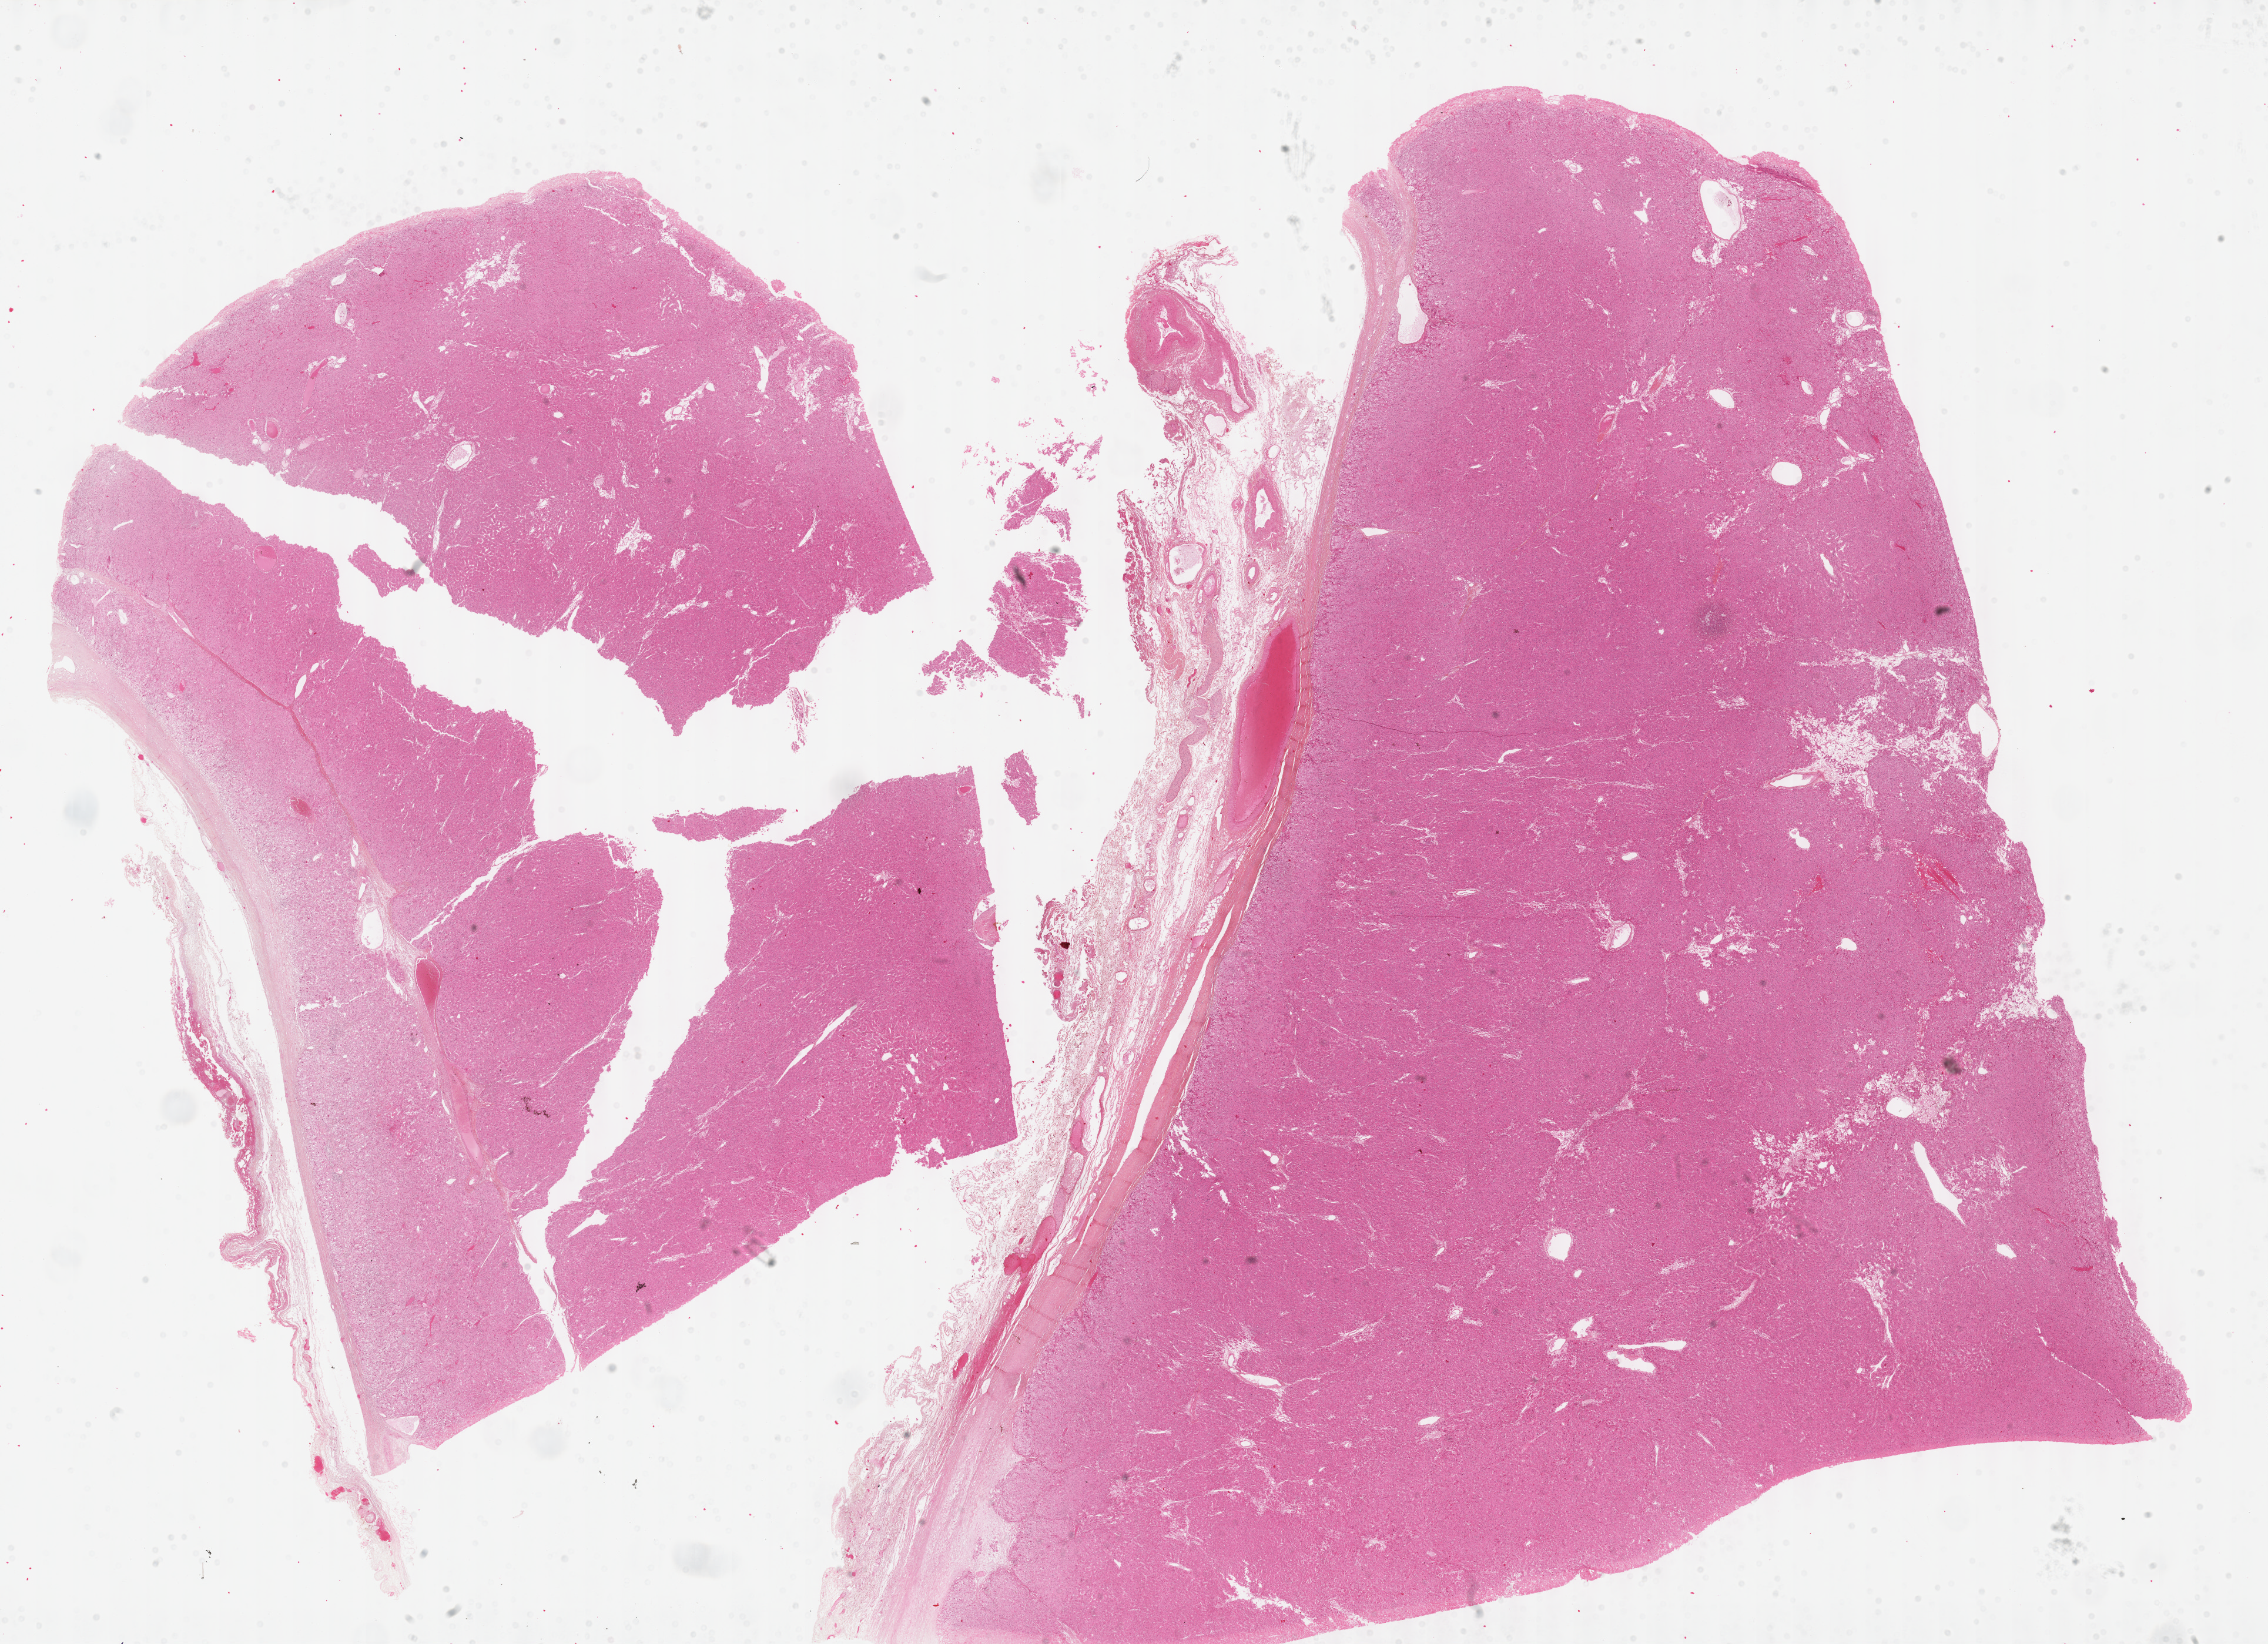
Whole-slide histology image, H&E-stained, shown as a low-resolution overview of the whole scanned area (about 31.2 x 22.6 mm, acquisition: 40x scan); formalin-fixed paraffin-embedded (FFPE) diagnostic section; sample: primary tumour, adrenal cortex. Patient: female, age at initial diagnosis 31 years.
Lymph nodes positive (case pathology): 0 of 10 examined. Pathologic diagnosis: Adrenal cortical carcinoma (cortex of adrenal gland).